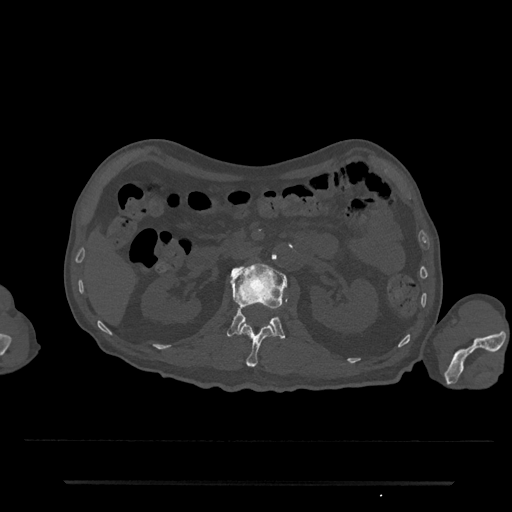
CT including the spine, one axial slice. Slice 95 of 797 in the series (ordered by position). Reconstruction kernel Br40s/3. 120 kVp. Bone window (W 1800 / L 400 HU). 512 × 512 image matrix, field of view 427 × 427 mm. Male patient, age 74 years. From the clinical record (not read from this slice): primary cancer: prostate.
Structures marked on this image (semi-automatic segmentation, software-assisted and operator-edited):
- L1 vertebra: bounding box (x1, y1, x2, y2) in pixels: (238, 322, 274, 367)
- L2 vertebra: (227, 263, 287, 339)